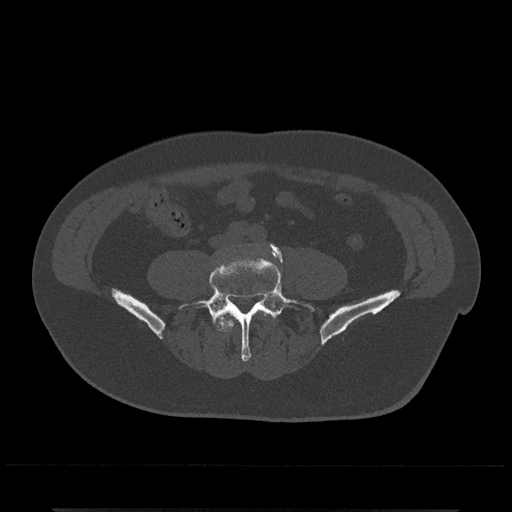
CT including the spine, one axial slice; position 102 of 797 along the scan axis; reconstruction kernel Br40s/3; 120 kVp; bone window (W 1800 / L 400 HU); 0.5 mm slice thickness; 512 × 512 image matrix. Male patient, age 67 years. Case-level facts recorded for this patient, not image findings: primary cancer: prostate.
Structures marked on this image (semi-automatically segmented with operator editing):
- L4 vertebra: bounding box (x1, y1, x2, y2) in pixels: (217, 311, 269, 332)
- L5 vertebra: (179, 244, 315, 361)